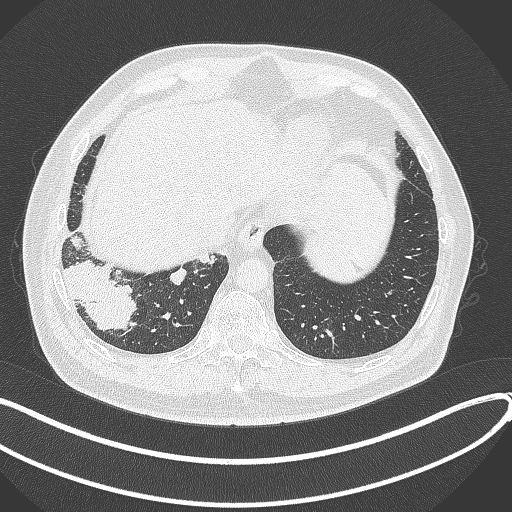
Chest CT, one axial slice. Position 68 of 360 along the scan axis. Reconstruction kernel B70f. Lung window (W 1500 / L -600 HU). 1 mm slice thickness. 512 × 512 image matrix. Patient: male, 59 years.
Outlined on this slice (bounding box drawn by a radiologist):
- lung tumour (recorded histology: adenocarcinoma): bounding box [x1, y1, x2, y2] px = [62, 257, 136, 336]